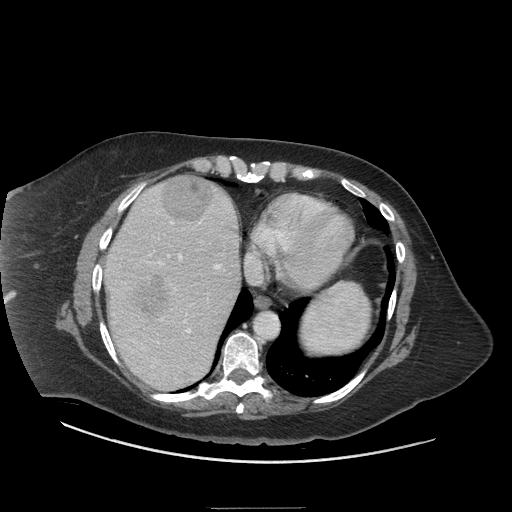
Contrast-enhanced abdominal CT (liver protocol), one axial slice. Position 58 of 81 along the scan axis. 140 kVp. Soft-tissue window (W 400 / L 40 HU). 512 × 512 image matrix. From the clinical record (not read from this slice): diagnosis: hepatocellular carcinoma (patient treated with transarterial chemoembolisation; whether this scan precedes or follows treatment is not stated here); TNM stage (as recorded): Stage-II; Child-Pugh class: A; tumour differentiation: moderately differentiated; tumour nodularity: multinodular.
Outlined on this slice (semi-automatically segmented with operator editing):
- abdominal aorta: bounding box <254,312,279,340> (left, top, right, bottom; pixels)
- liver parenchyma outside the tumour (the mass and vessels are separate outlines, so this box may not span the whole liver): <104,176,240,390>
- mass: <129,175,212,319>
- liver vessels: <112,200,222,367>